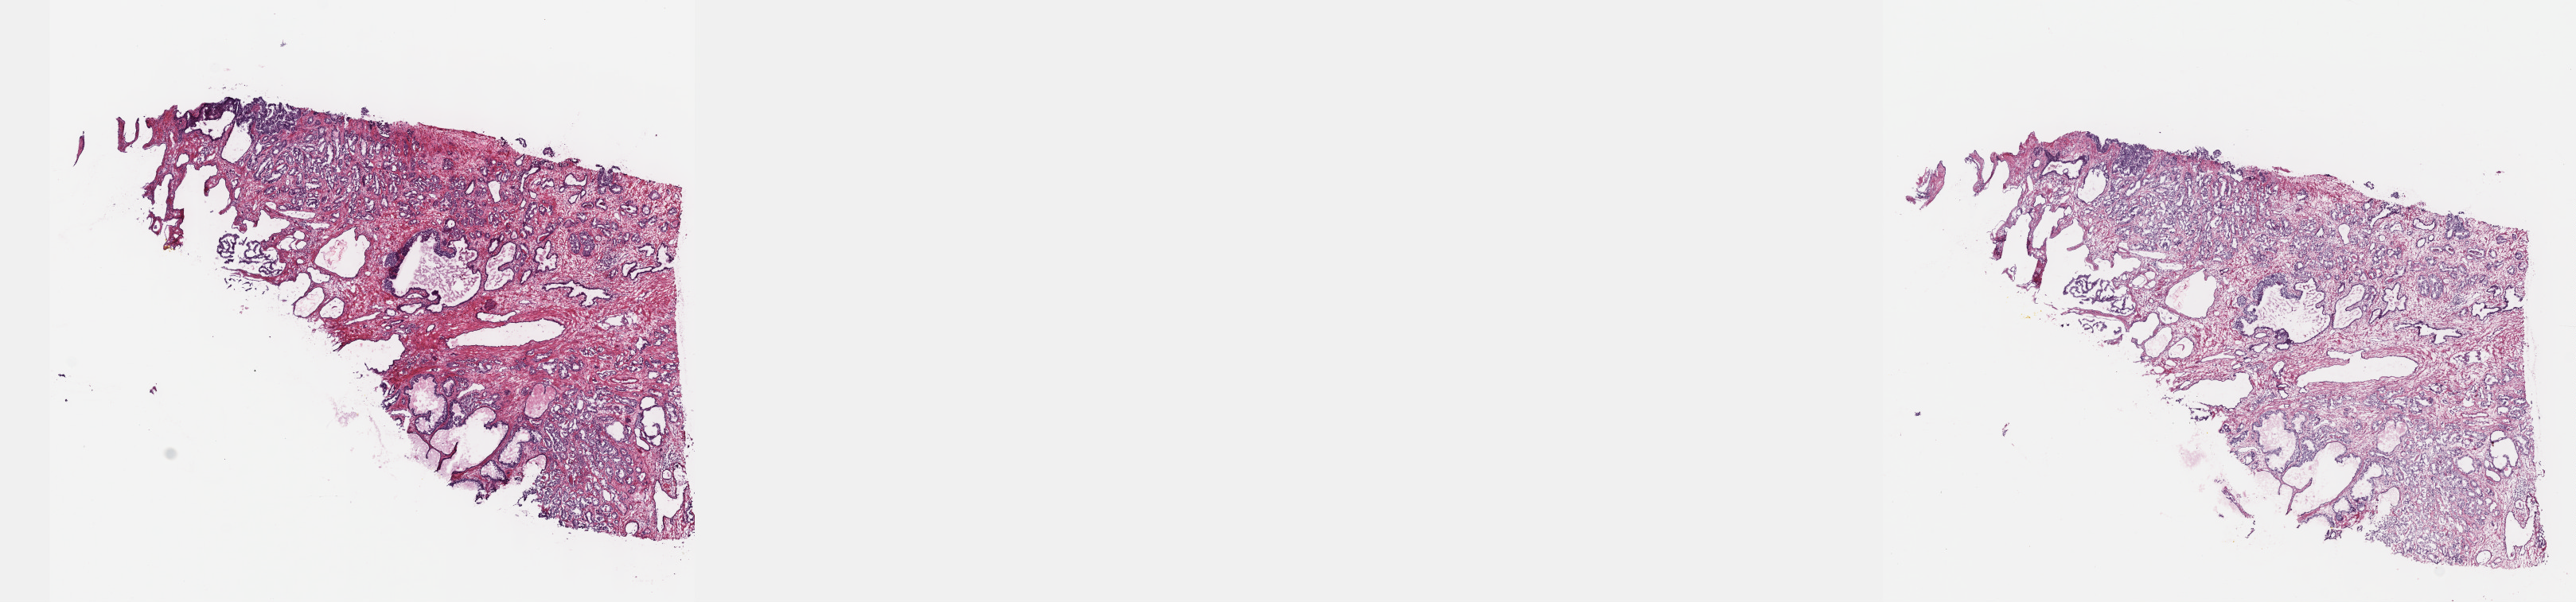
Whole-slide histology image, Hematoxylin and eosin (H&E) stained, shown as a low-resolution overview of the whole scanned area (about 26.2 x 6.1 mm). Frozen section from the top of the tissue portion. Sample: primary tumour, prostate. Male, age 63 years at initial diagnosis. Gleason score: 7 (3+4). Composition of this section per pathologist review: tumour cells 70%, tumour nuclei 70%, normal cells 10%, stromal cells 20%, necrosis 0%. Inflammatory infiltration, as recorded: lymphocyte infiltration 0%, monocyte infiltration 0%, neutrophil infiltration 0%.
Lymph nodes positive (case pathology): 0 of 23 examined. Histologic diagnosis: Adenocarcinoma, NOS. Laterality: bilateral.